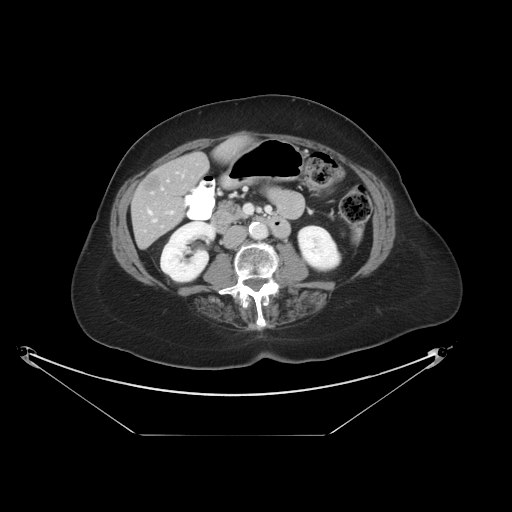
Contrast-enhanced abdominal CT, one axial slice. Position 10 of 36 along the scan axis. Reconstruction kernel STANDARD. 120 kVp. Intravenous contrast given. Soft-tissue window (W 400 / L 40 HU). 5 mm slice thickness. 512 × 512 image matrix, field of view 500 × 500 mm. Female patient, age 70 years. Case-level facts recorded for this patient, not image findings: diagnosis: colorectal cancer liver metastases, imaged before liver resection; multiple liver metastases: no; largest metastasis: 2.5 cm; disease in both lobes: no.
Outlined on this slice (manually delineated by an expert):
- hepatic veins: bounding box <148,211,157,222> (left, top, right, bottom; pixels)
- liver: <133,141,240,246>
- planned liver remnant (the part of the liver to remain after resection): <136,142,240,244>
- portal vein (with intrahepatic branches): <162,189,173,214>
- liver metastasis: <142,173,163,194>